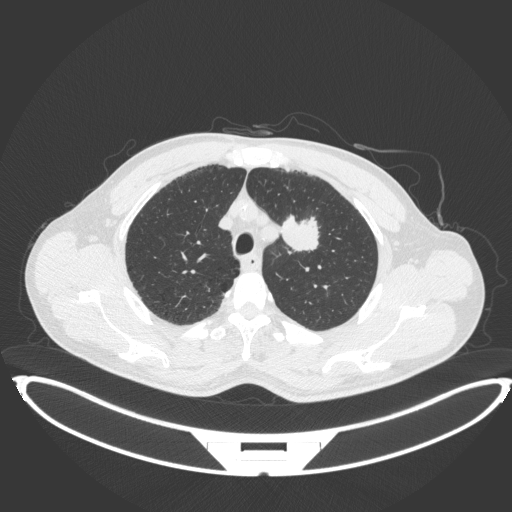
Chest CT, one axial slice. Slice 345 of 407 in the series (ordered by position). Reconstruction kernel B31f. 120 kVp. Lung window (W 1500 / L -600 HU). 512 × 512 image matrix, field of view 457 × 457 mm. Male patient, age 60 years. Case-level facts recorded for this patient, not image findings: clinical TNM (as recorded): T2a N0 M0; histopathological grade: G1-G2.
Outlined on this slice (bounding box drawn by a radiologist):
- lung tumour (recorded histology: squamous cell carcinoma): box from (x=278, y=212) to (x=322, y=255) px